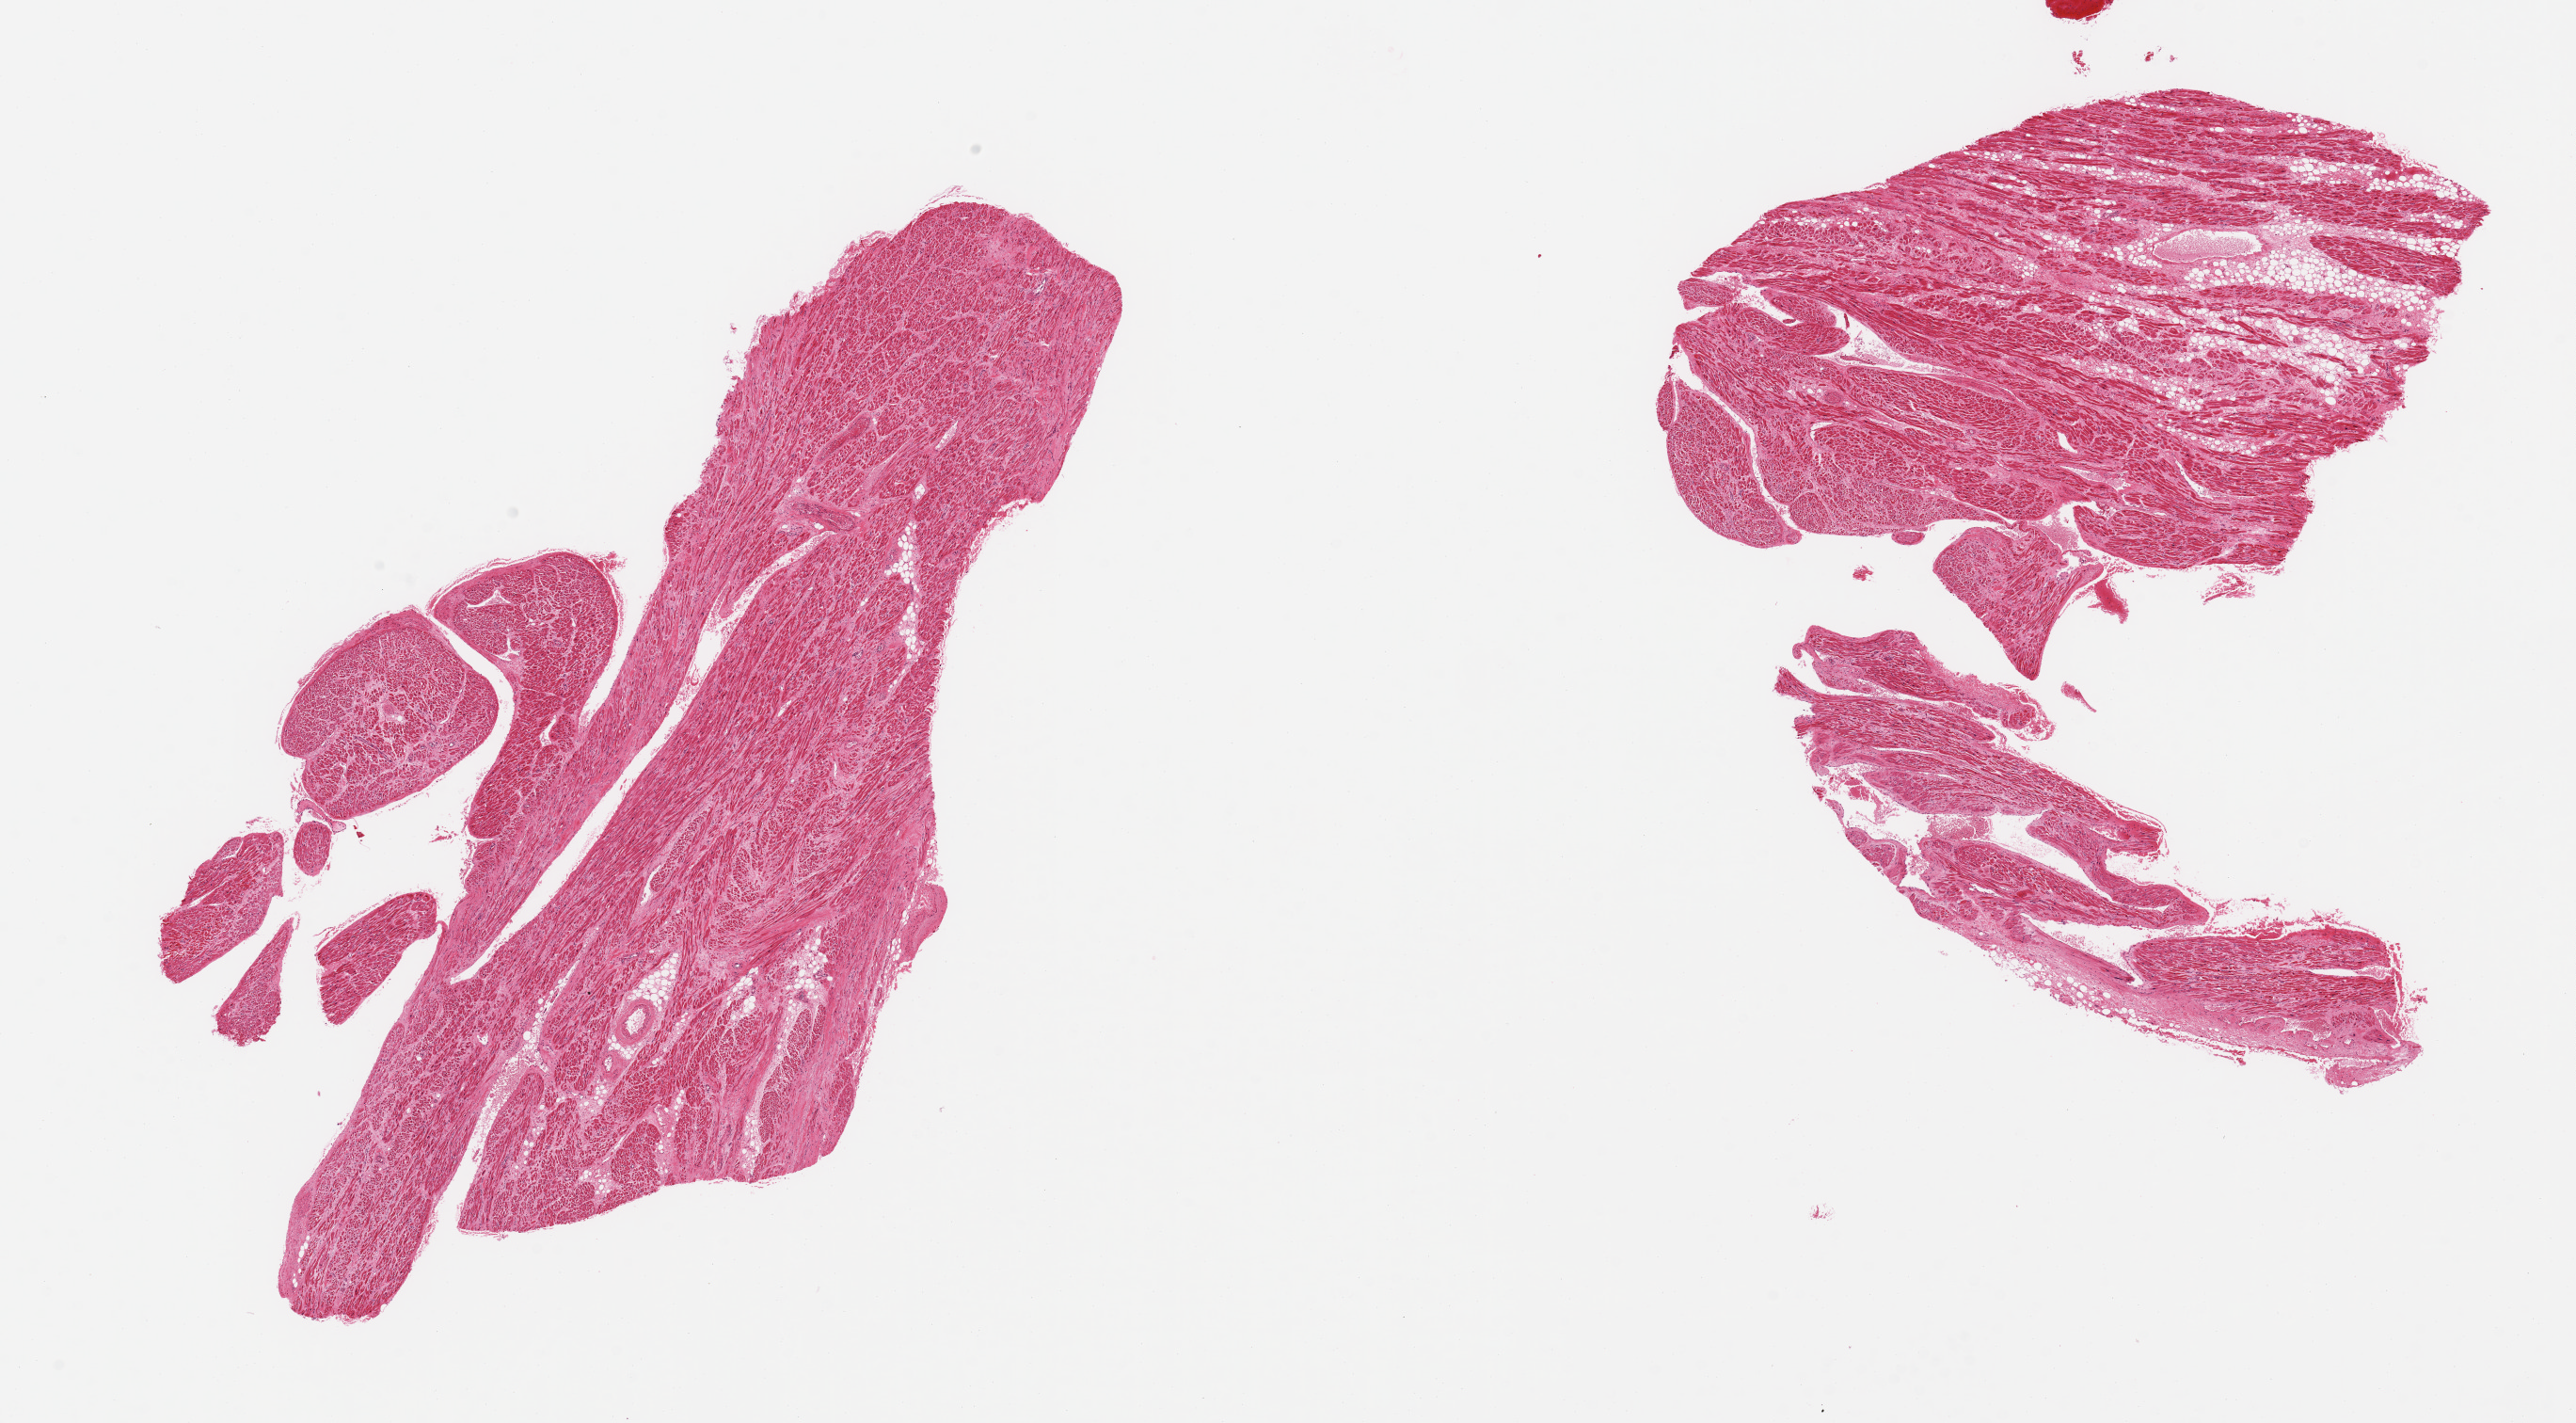
Hematoxylin and eosin (H&E) whole-slide image, brightfield — a low-resolution overview of the entire scanned area, about 21.7 x 12.0 mm. PAXgene-fixed paraffin-embedded (PFPE) section. Sampled site (target tissue): auricular appendage. Donor tissue sample. Donor sex: male.
• reviewer comment on this tissue sample: 2 pieces; 10% internal fat